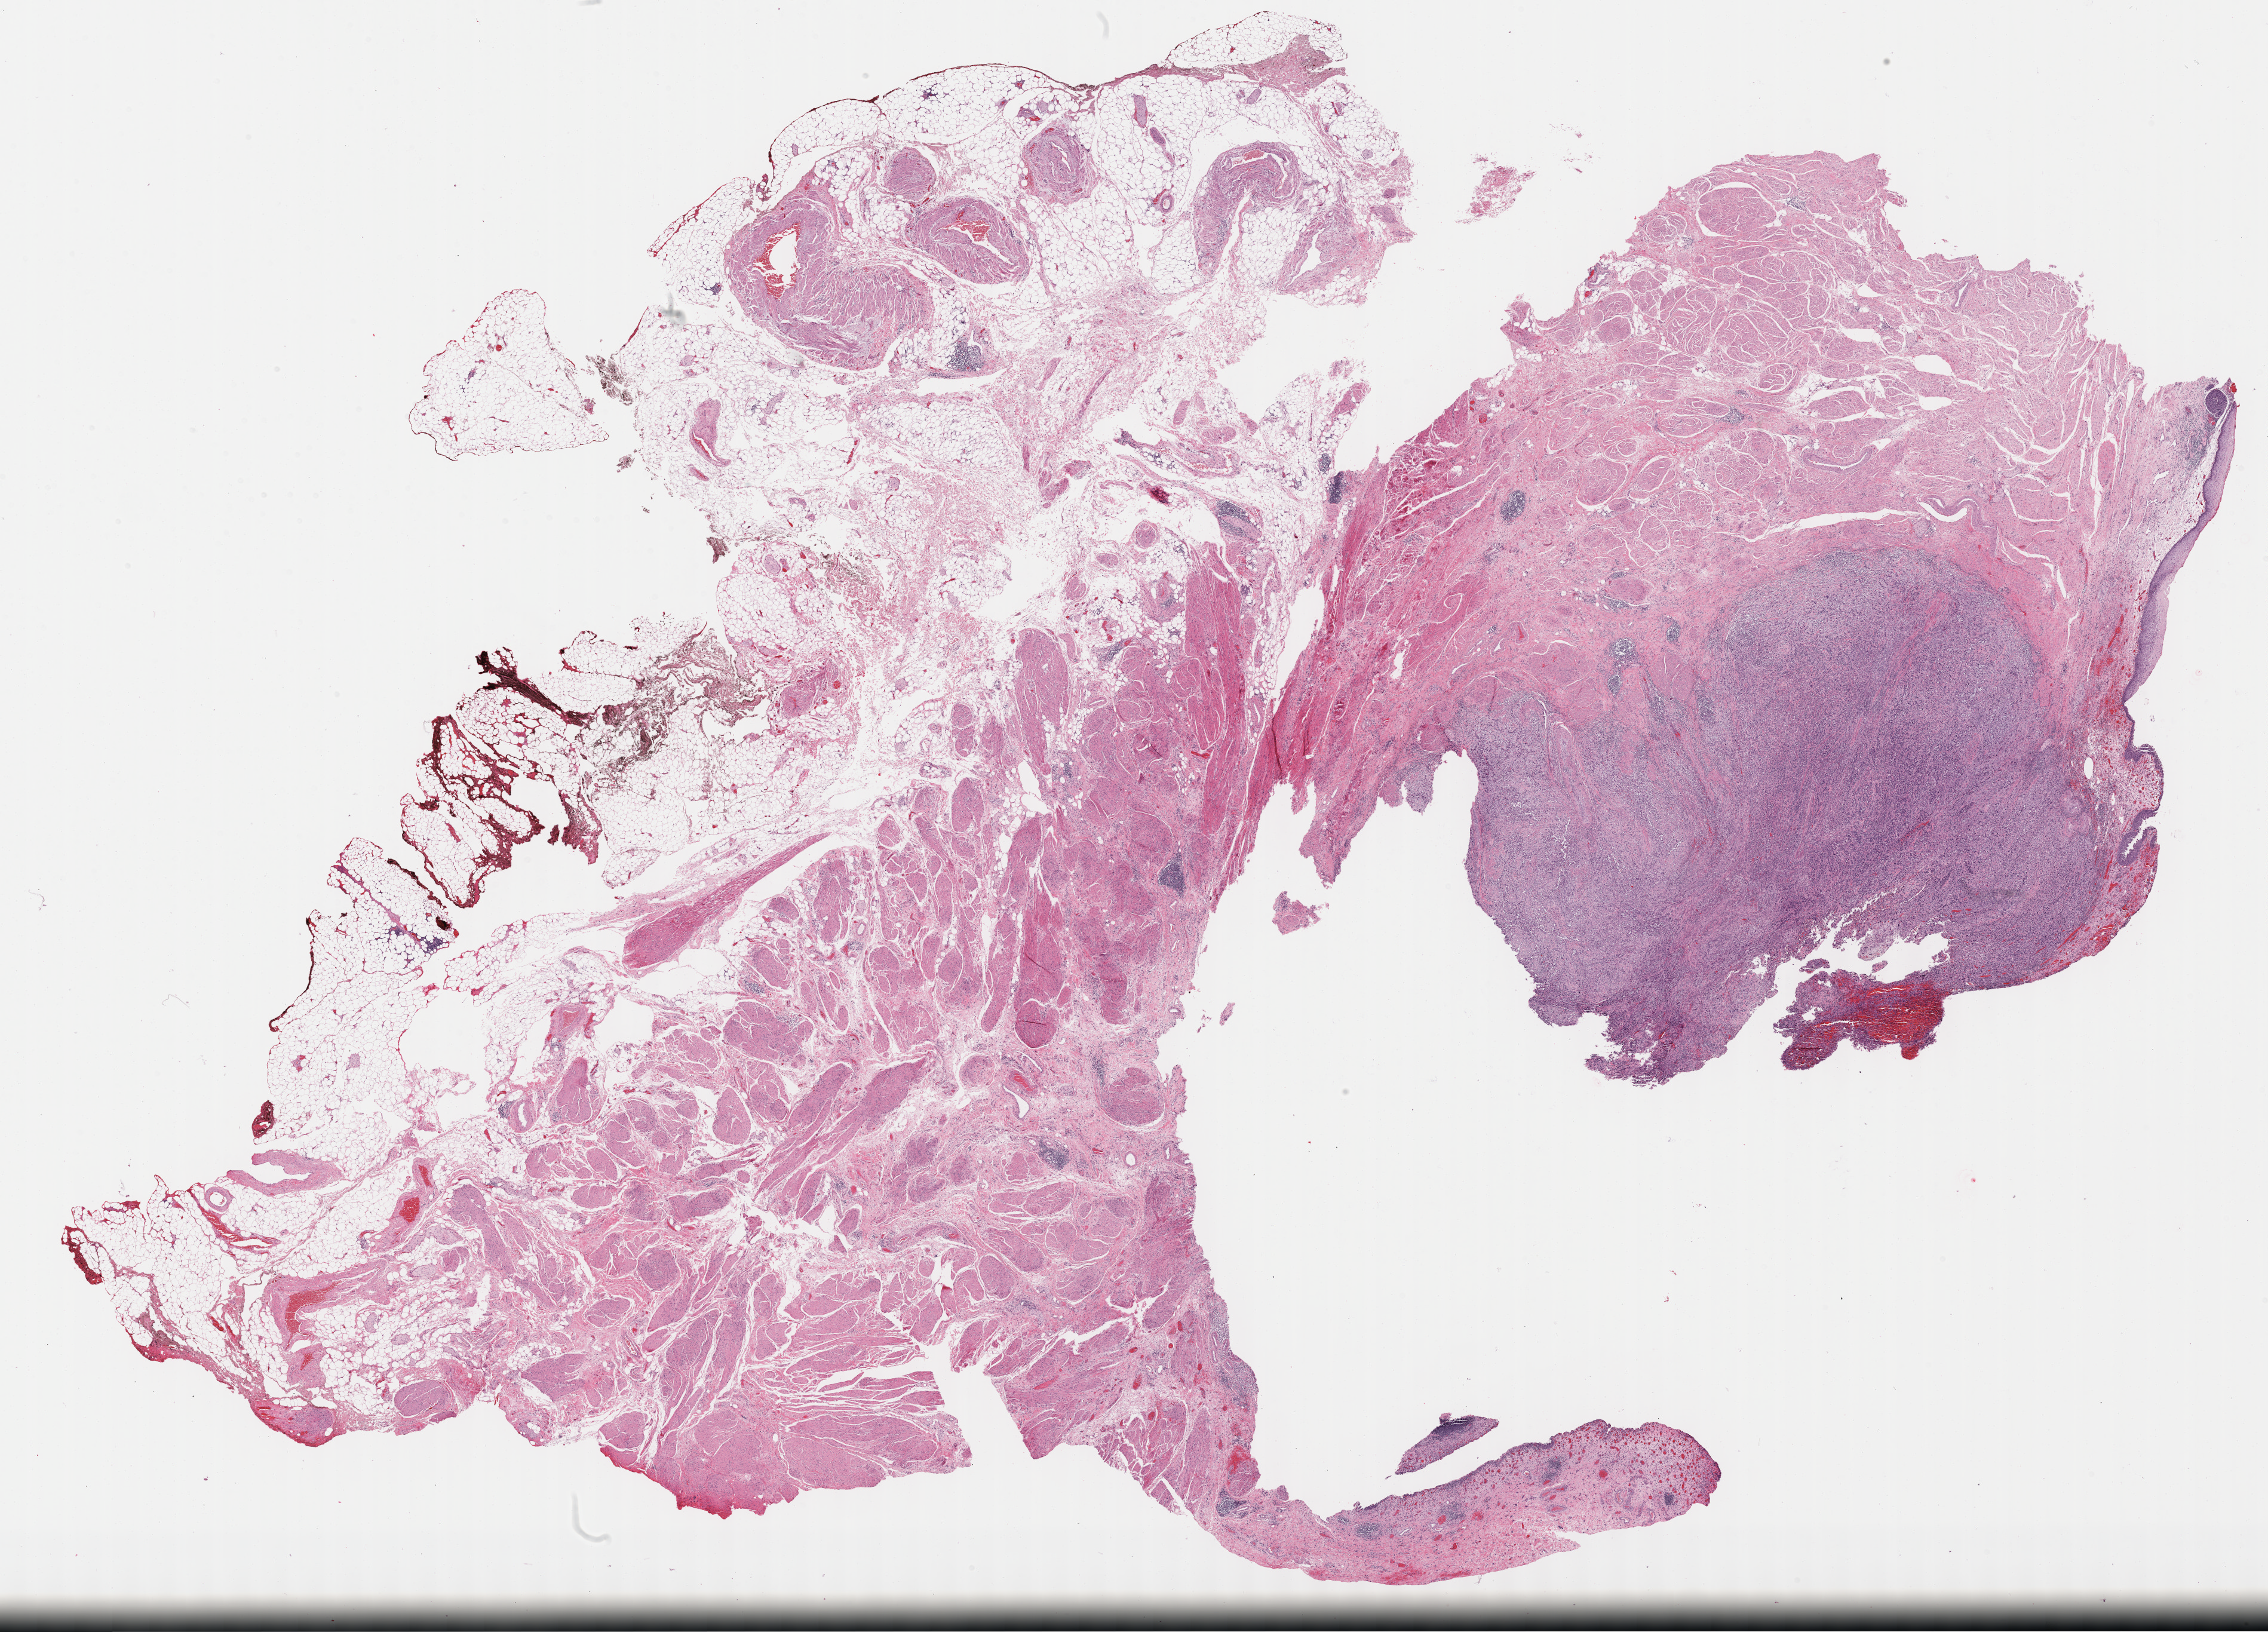
Hematoxylin and eosin (H&E) stained whole-slide image — shown as a low-resolution overview of the whole scanned area (about 30.7 x 22.1 mm); formalin-fixed paraffin-embedded (FFPE) diagnostic section; sample: primary tumour, bladder. Female patient; age at initial diagnosis 82 years. Histologic grade: high grade.
* AJCC pathologic stage: II (6th edition)
* histologic diagnosis: Transitional cell carcinoma